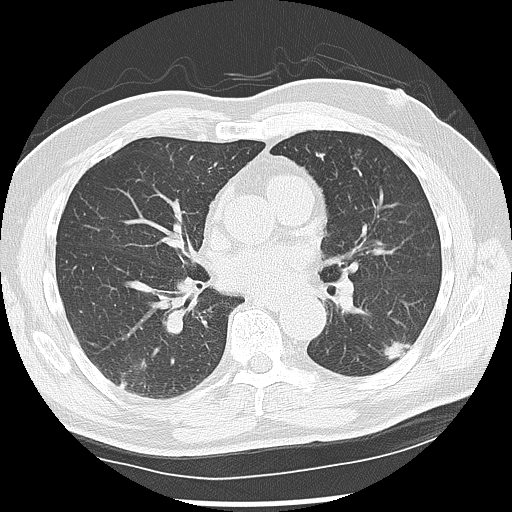
Low-dose screening chest CT, one axial slice. Position 64 of 142 along the scan axis. Reconstruction kernel LUNG. Lung window (W 1500 / L -600 HU). 2.5 mm slice thickness. 512 × 512 image matrix, field of view 360 × 360 mm.
Structures marked on this image (expert manual segmentation):
- lesion 1 (nodule, lower lobe of left lung): bounding box [x1, y1, x2, y2] px = [383, 341, 411, 361]